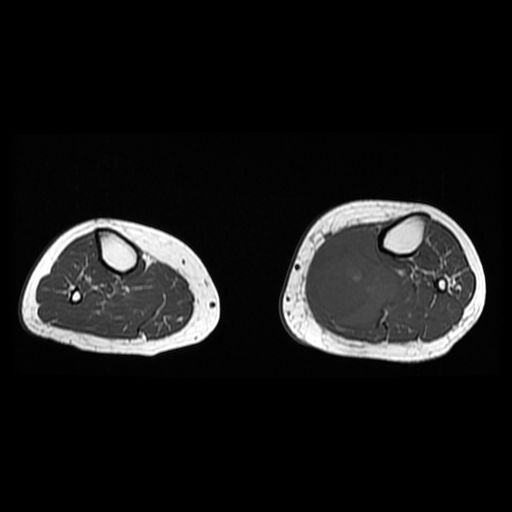
MRI of an extremity soft-tissue mass, one axial slice. Slice 17 of 38 in the series (ordered by position). 512 × 512 image matrix, field of view 330 × 330 mm. Female patient. Case-level facts recorded for this patient, not image findings: histological type: extraskeletal high grade osteogenic sarcoma; grade: high; site of the primary tumour: left calf.
Annotated regions visible in this slice (outlined manually by an expert reader):
- gross tumour volume (mass): bounding box <308,228,399,325> (left, top, right, bottom; pixels)